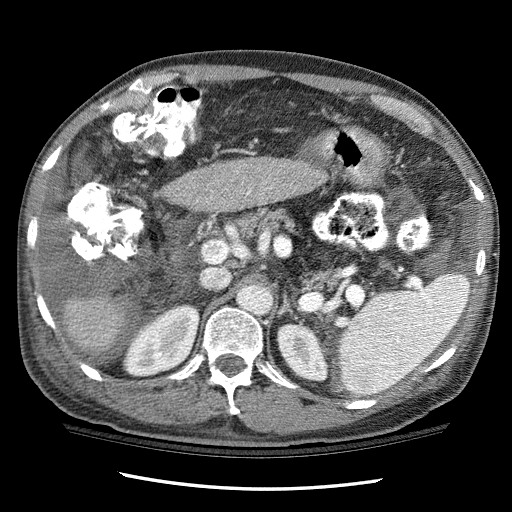
Contrast-enhanced abdominal CT (liver protocol), one axial slice; position 57 of 114 along the scan axis; reconstruction kernel STANDARD; 120 kVp; one of 3 acquisitions stored at this slice position; soft-tissue window (W 400 / L 40 HU); 2.5 mm slice thickness; 512 × 512 image matrix, field of view 360 × 360 mm. From the clinical record (not read from this slice): diagnosis: hepatocellular carcinoma (patient treated with transarterial chemoembolisation; whether this scan precedes or follows treatment is not stated here); TNM stage (as recorded): Stage-I; Child-Pugh class: C; tumour differentiation: well differentiated; tumour nodularity: uninodular.
Annotated regions visible in this slice (semi-automatically segmented with operator editing):
- liver parenchyma outside the tumour (the mass and vessels are separate outlines, so this box may not span the whole liver): bounding box (x1, y1, x2, y2) in pixels: (68, 160, 326, 350)